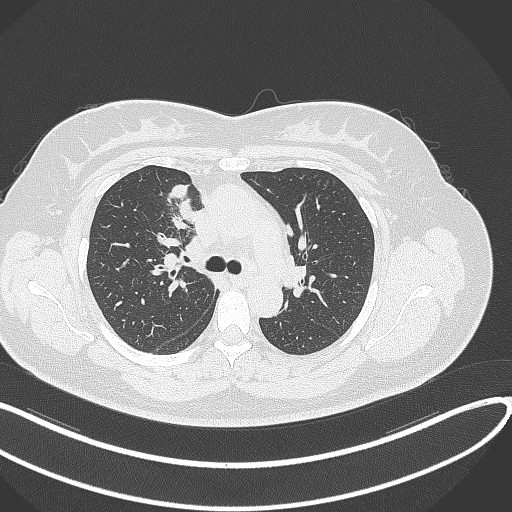
Chest CT, one axial slice; slice 187 of 303 in the series (ordered by position); reconstruction kernel B70f; lung window (W 1500 / L -600 HU); 1 mm slice thickness; 512 × 512 image matrix, field of view 400 × 400 mm. Patient: female, 46 years. Case-level facts recorded for this patient, not image findings: clinical TNM (as recorded): T2a N1 M0.
Structures marked on this image (bounding box drawn by a radiologist):
- lung tumour (recorded histology: adenocarcinoma): bounding box <163,183,198,227> (left, top, right, bottom; pixels)